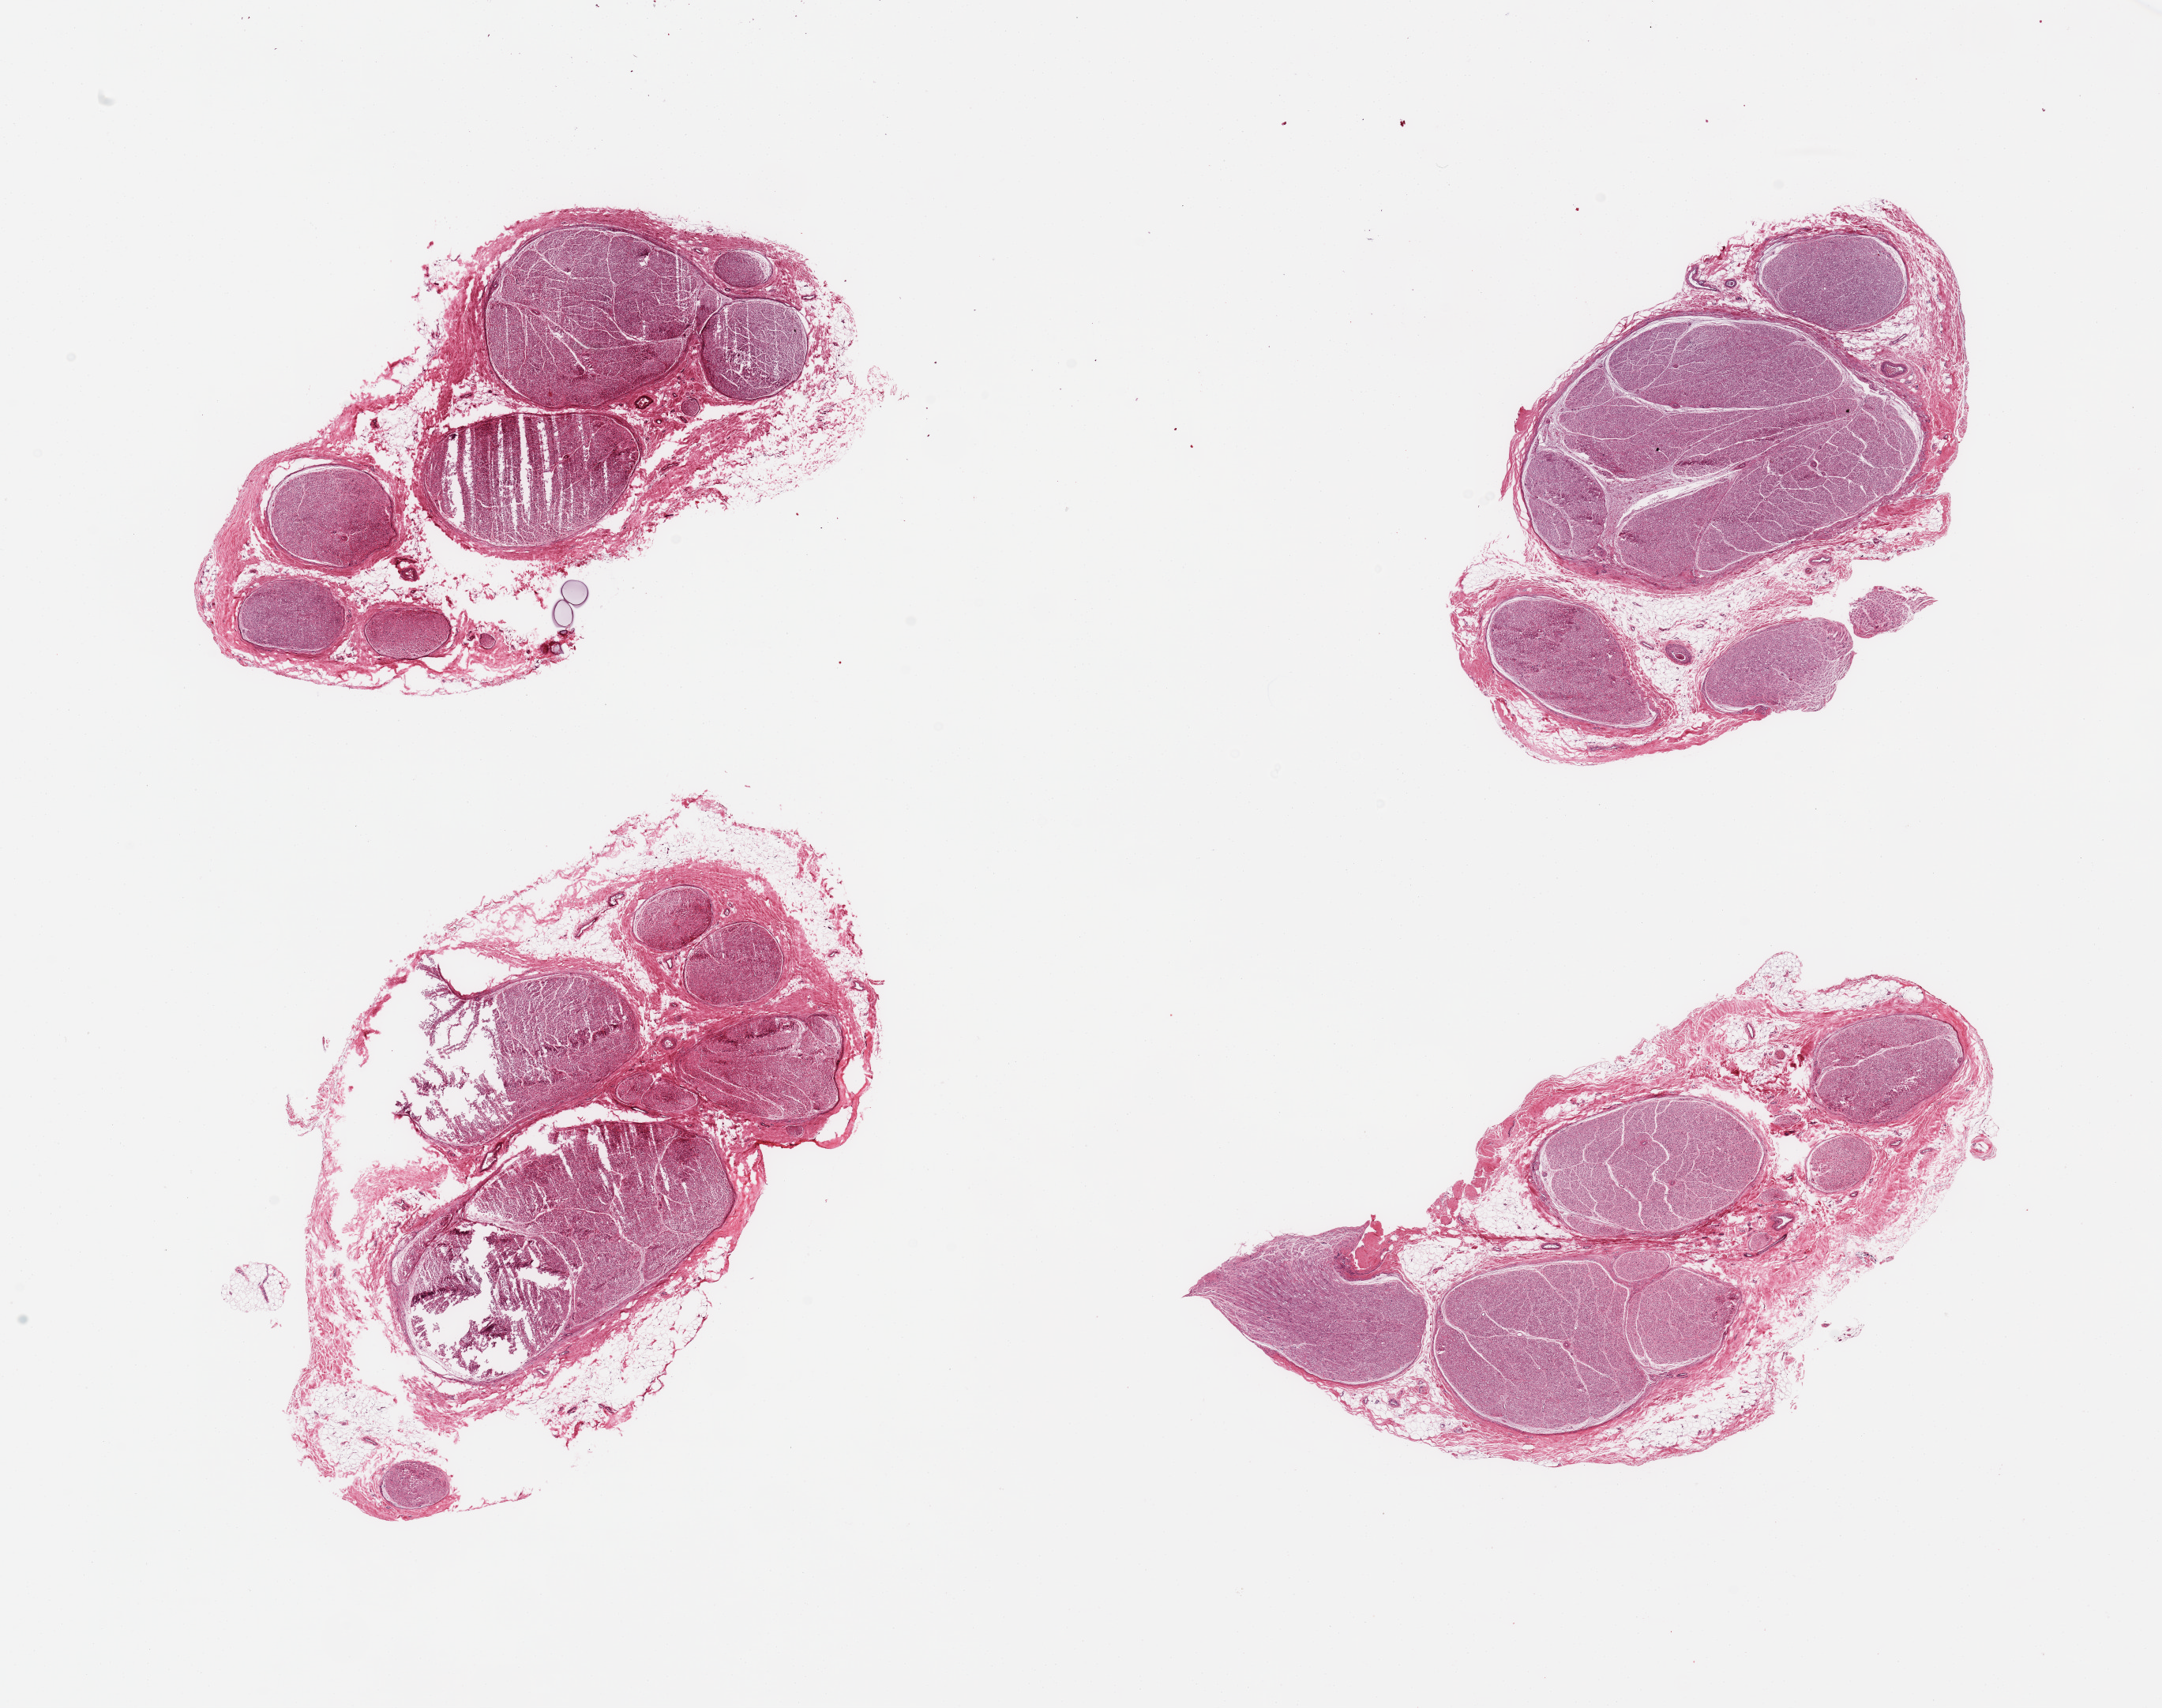
Haematoxylin and eosin whole-slide image, brightfield — shown as a low-resolution overview of the whole scanned area (about 21.7 x 17.1 mm, from a 20x scan). PAXgene-fixed, paraffin-embedded tissue. Sampled site (target tissue): tibial nerve. Donor tissue sample. Donor: male.
• review note (as recorded): 4 pieces; incomplete sections, include 20-40% attached and internal fat